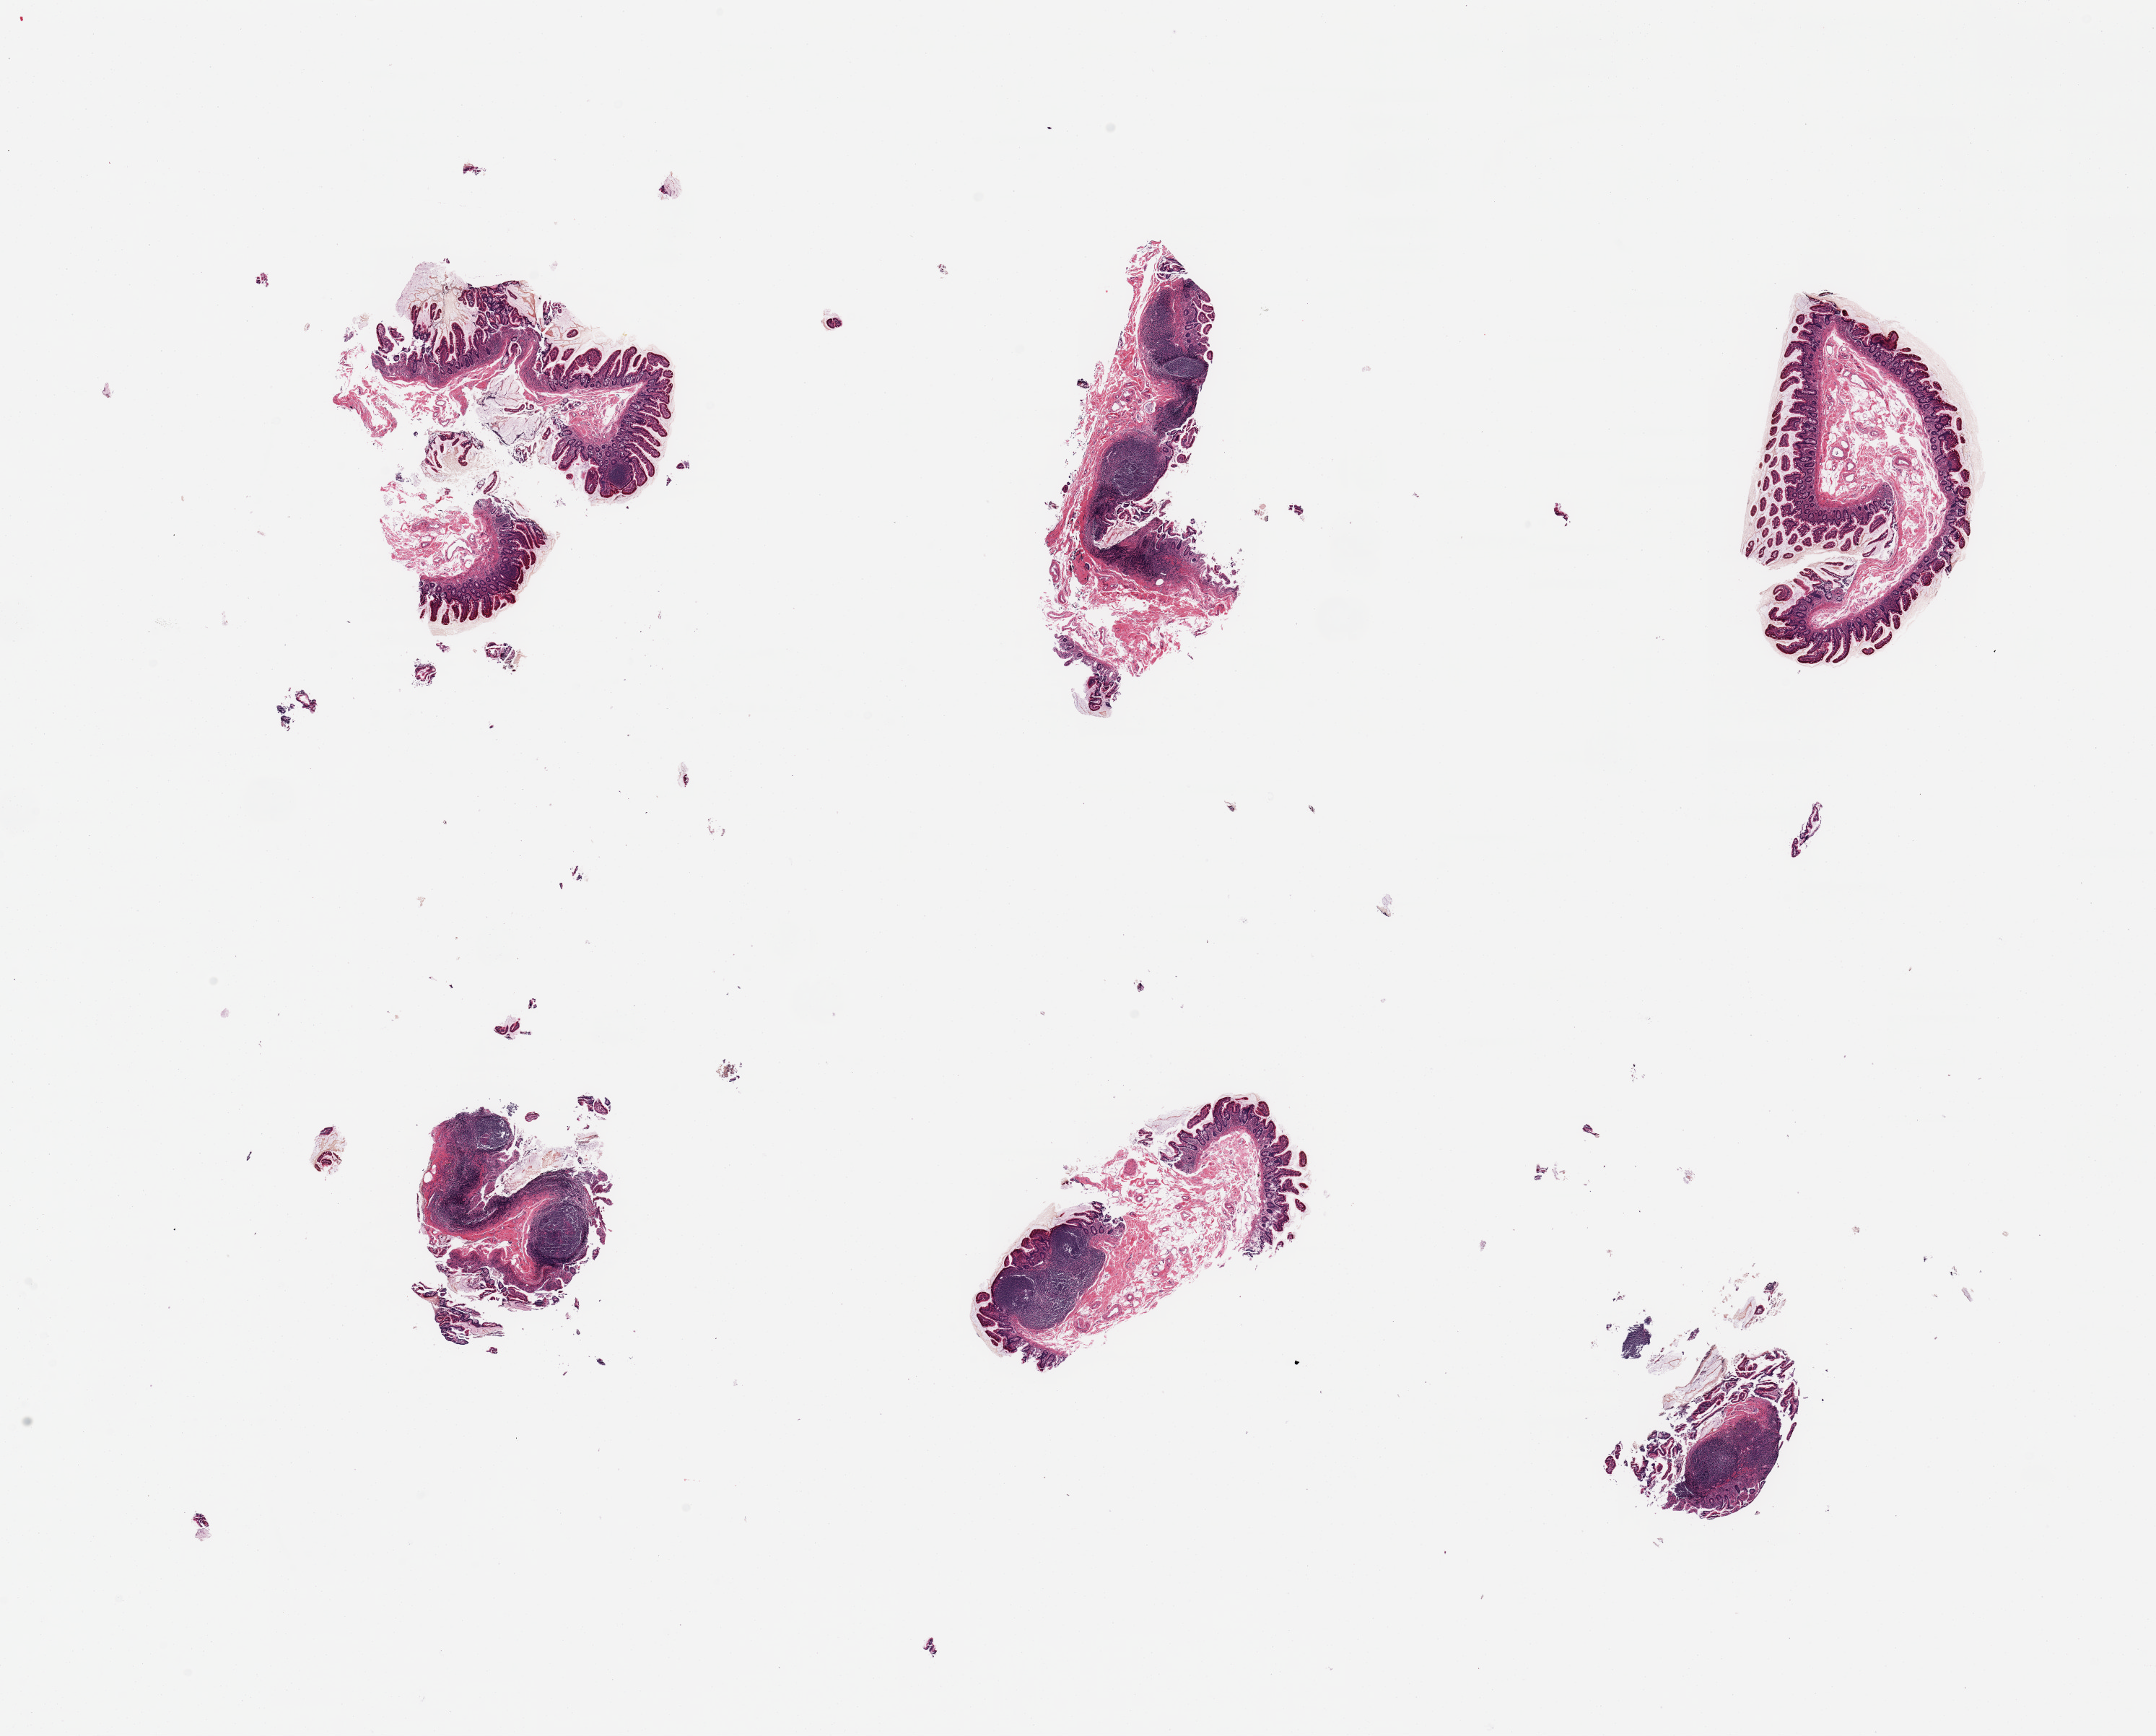
Digitized haematoxylin and eosin-stained section, brightfield, low-resolution overview of the scanned area, about 23.6 x 19.0 mm; PAXgene-fixed paraffin-embedded (PFPE) section; sampled site (target tissue): ileum; donor tissue sample. Donor: male.
Pathologist's review note for this sample: 6 pieces; mild to moderate autolysis; preserved target lymphoid aggregates.